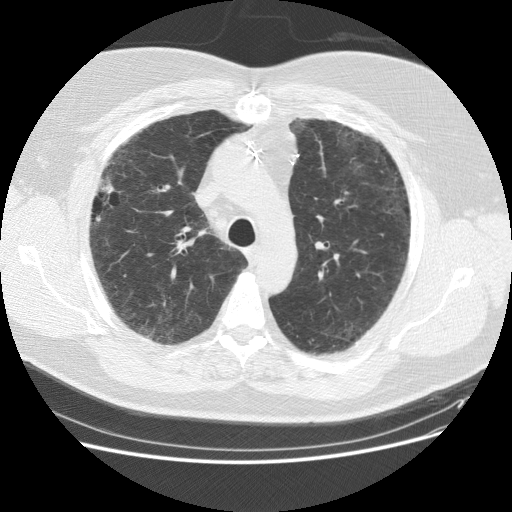
Low-dose screening chest CT, one axial slice; position 114 of 151 along the scan axis; 120 kVp; lung window (W 1500 / L -600 HU); 512 × 512 image matrix, field of view 378 × 378 mm.
Annotated regions visible in this slice (expert manual segmentation):
- lesion 2 (tumor, upper lobe of right lung): bounding box <97,178,114,198> (left, top, right, bottom; pixels)